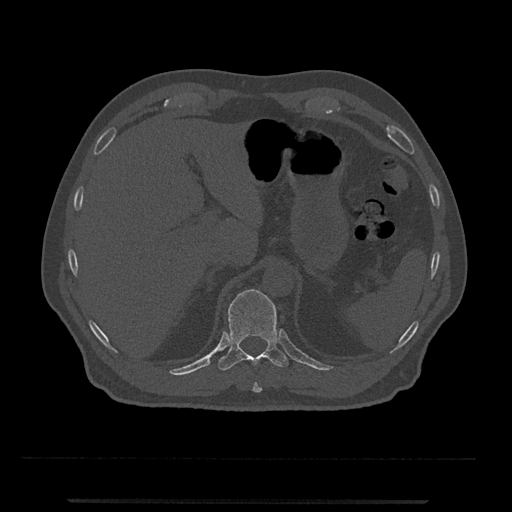
CT including the spine, one axial slice. Position 474 of 797 along the scan axis. Reconstruction kernel Br40s/3. 120 kVp. Bone window (W 1800 / L 400 HU). 0.5 mm slice thickness. 512 × 512 image matrix, field of view 419 × 419 mm. Male patient, age 63 years. Case-level facts recorded for this patient, not image findings: primary cancer: prostate.
Outlined on this slice (semi-automatic segmentation, software-assisted and operator-edited):
- T10 vertebra: box from (x=252, y=382) to (x=262, y=393) px
- T11 vertebra: (x=218, y=289)–(x=289, y=371)